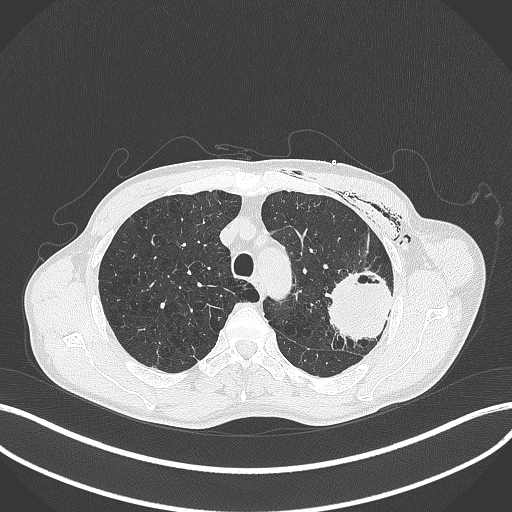
Chest CT, one axial slice. Slice 311 of 457 in the series (ordered by position). Lung window (W 1500 / L -600 HU). 512 × 512 image matrix, field of view 400 × 400 mm. Male patient, age 58 years. From the clinical record (not read from this slice): clinical TNM (as recorded): T3 N0 M0.
Structures marked on this image (bounding box drawn by a radiologist):
- lung tumour (recorded histology: adenocarcinoma): bounding box [x1, y1, x2, y2] px = [326, 267, 397, 343]